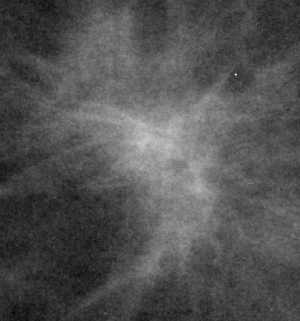
Cropped region of a digitized screen-film mammogram centred on a radiologist-marked abnormality, right breast, MLO view, BI-RADS breast density category 1 (scale 1–4).
- Marked abnormality: mass, shape irregular / architectural distortion, margins spiculated; BI-RADS assessment category 5; subtlety rating 5 on a 1 (subtle) to 5 (obvious) scale; pathology (as recorded): malignant.